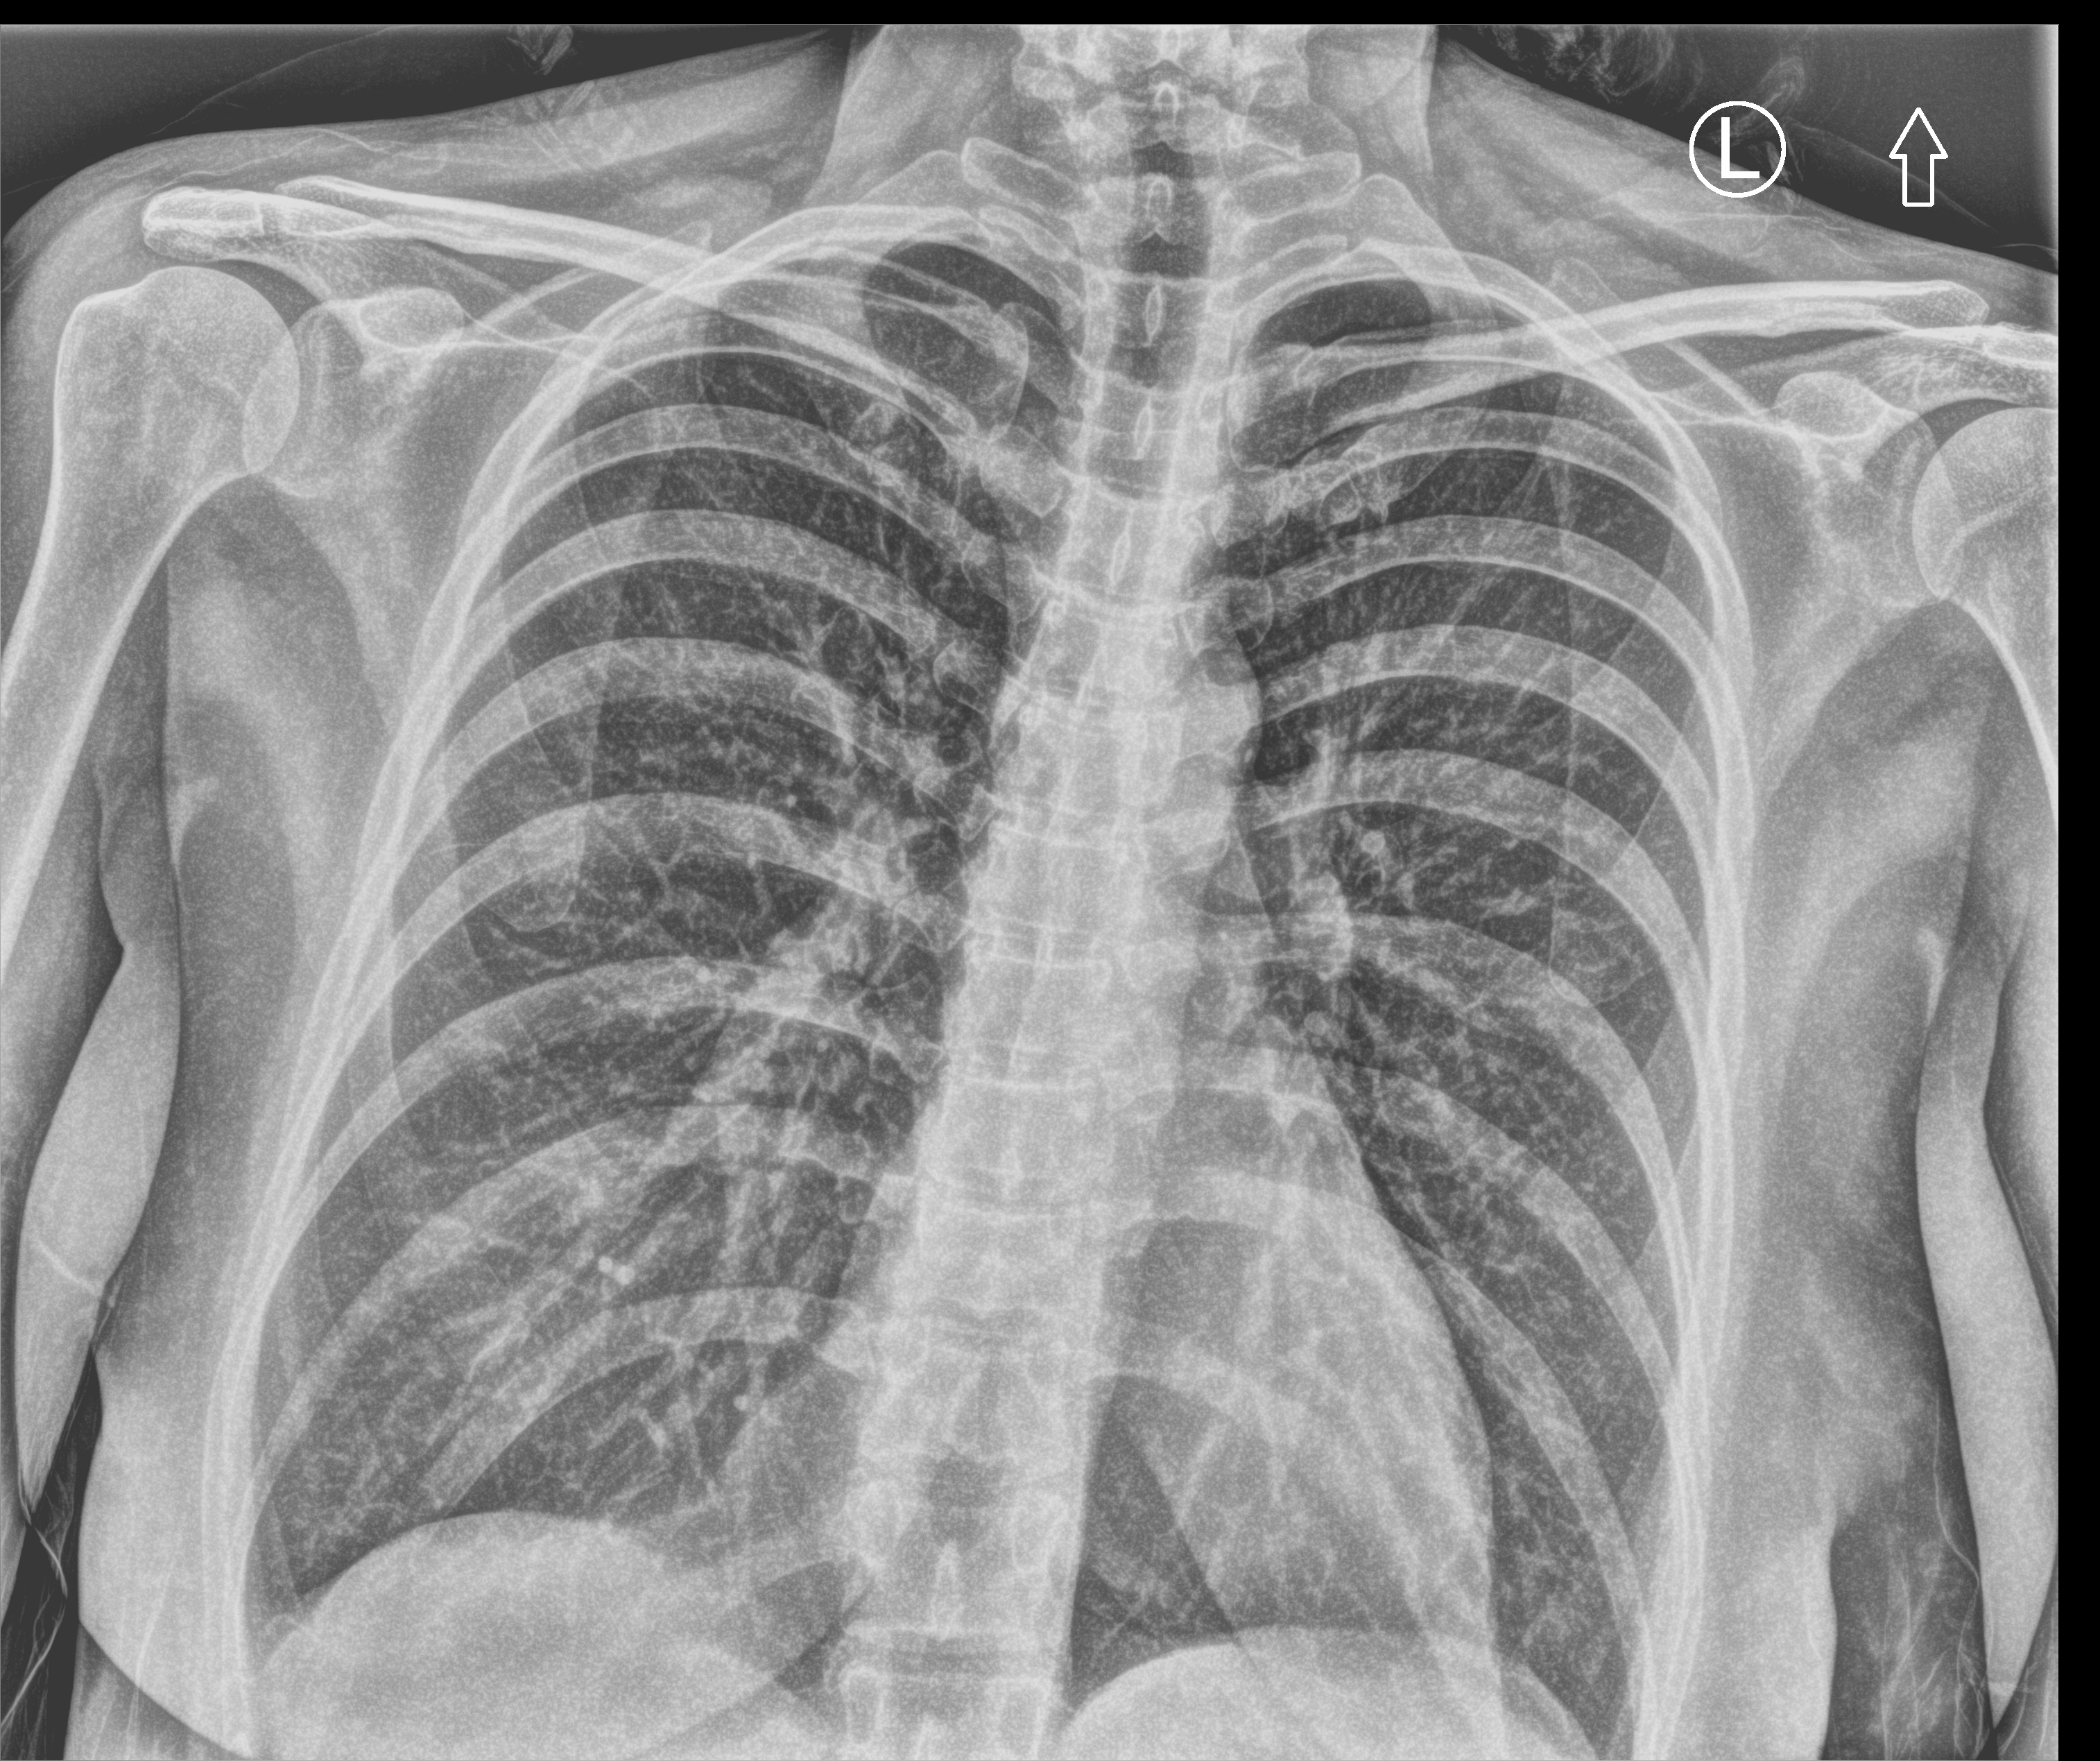
Portable chest radiograph, anteroposterior (AP) projection. Patient hospitalised with COVID-19; female, aged 18–59 years.
Admission-level facts for this patient (not findings on this image; timing relative to this image not recorded):
- mechanically ventilated during this hospital stay: no